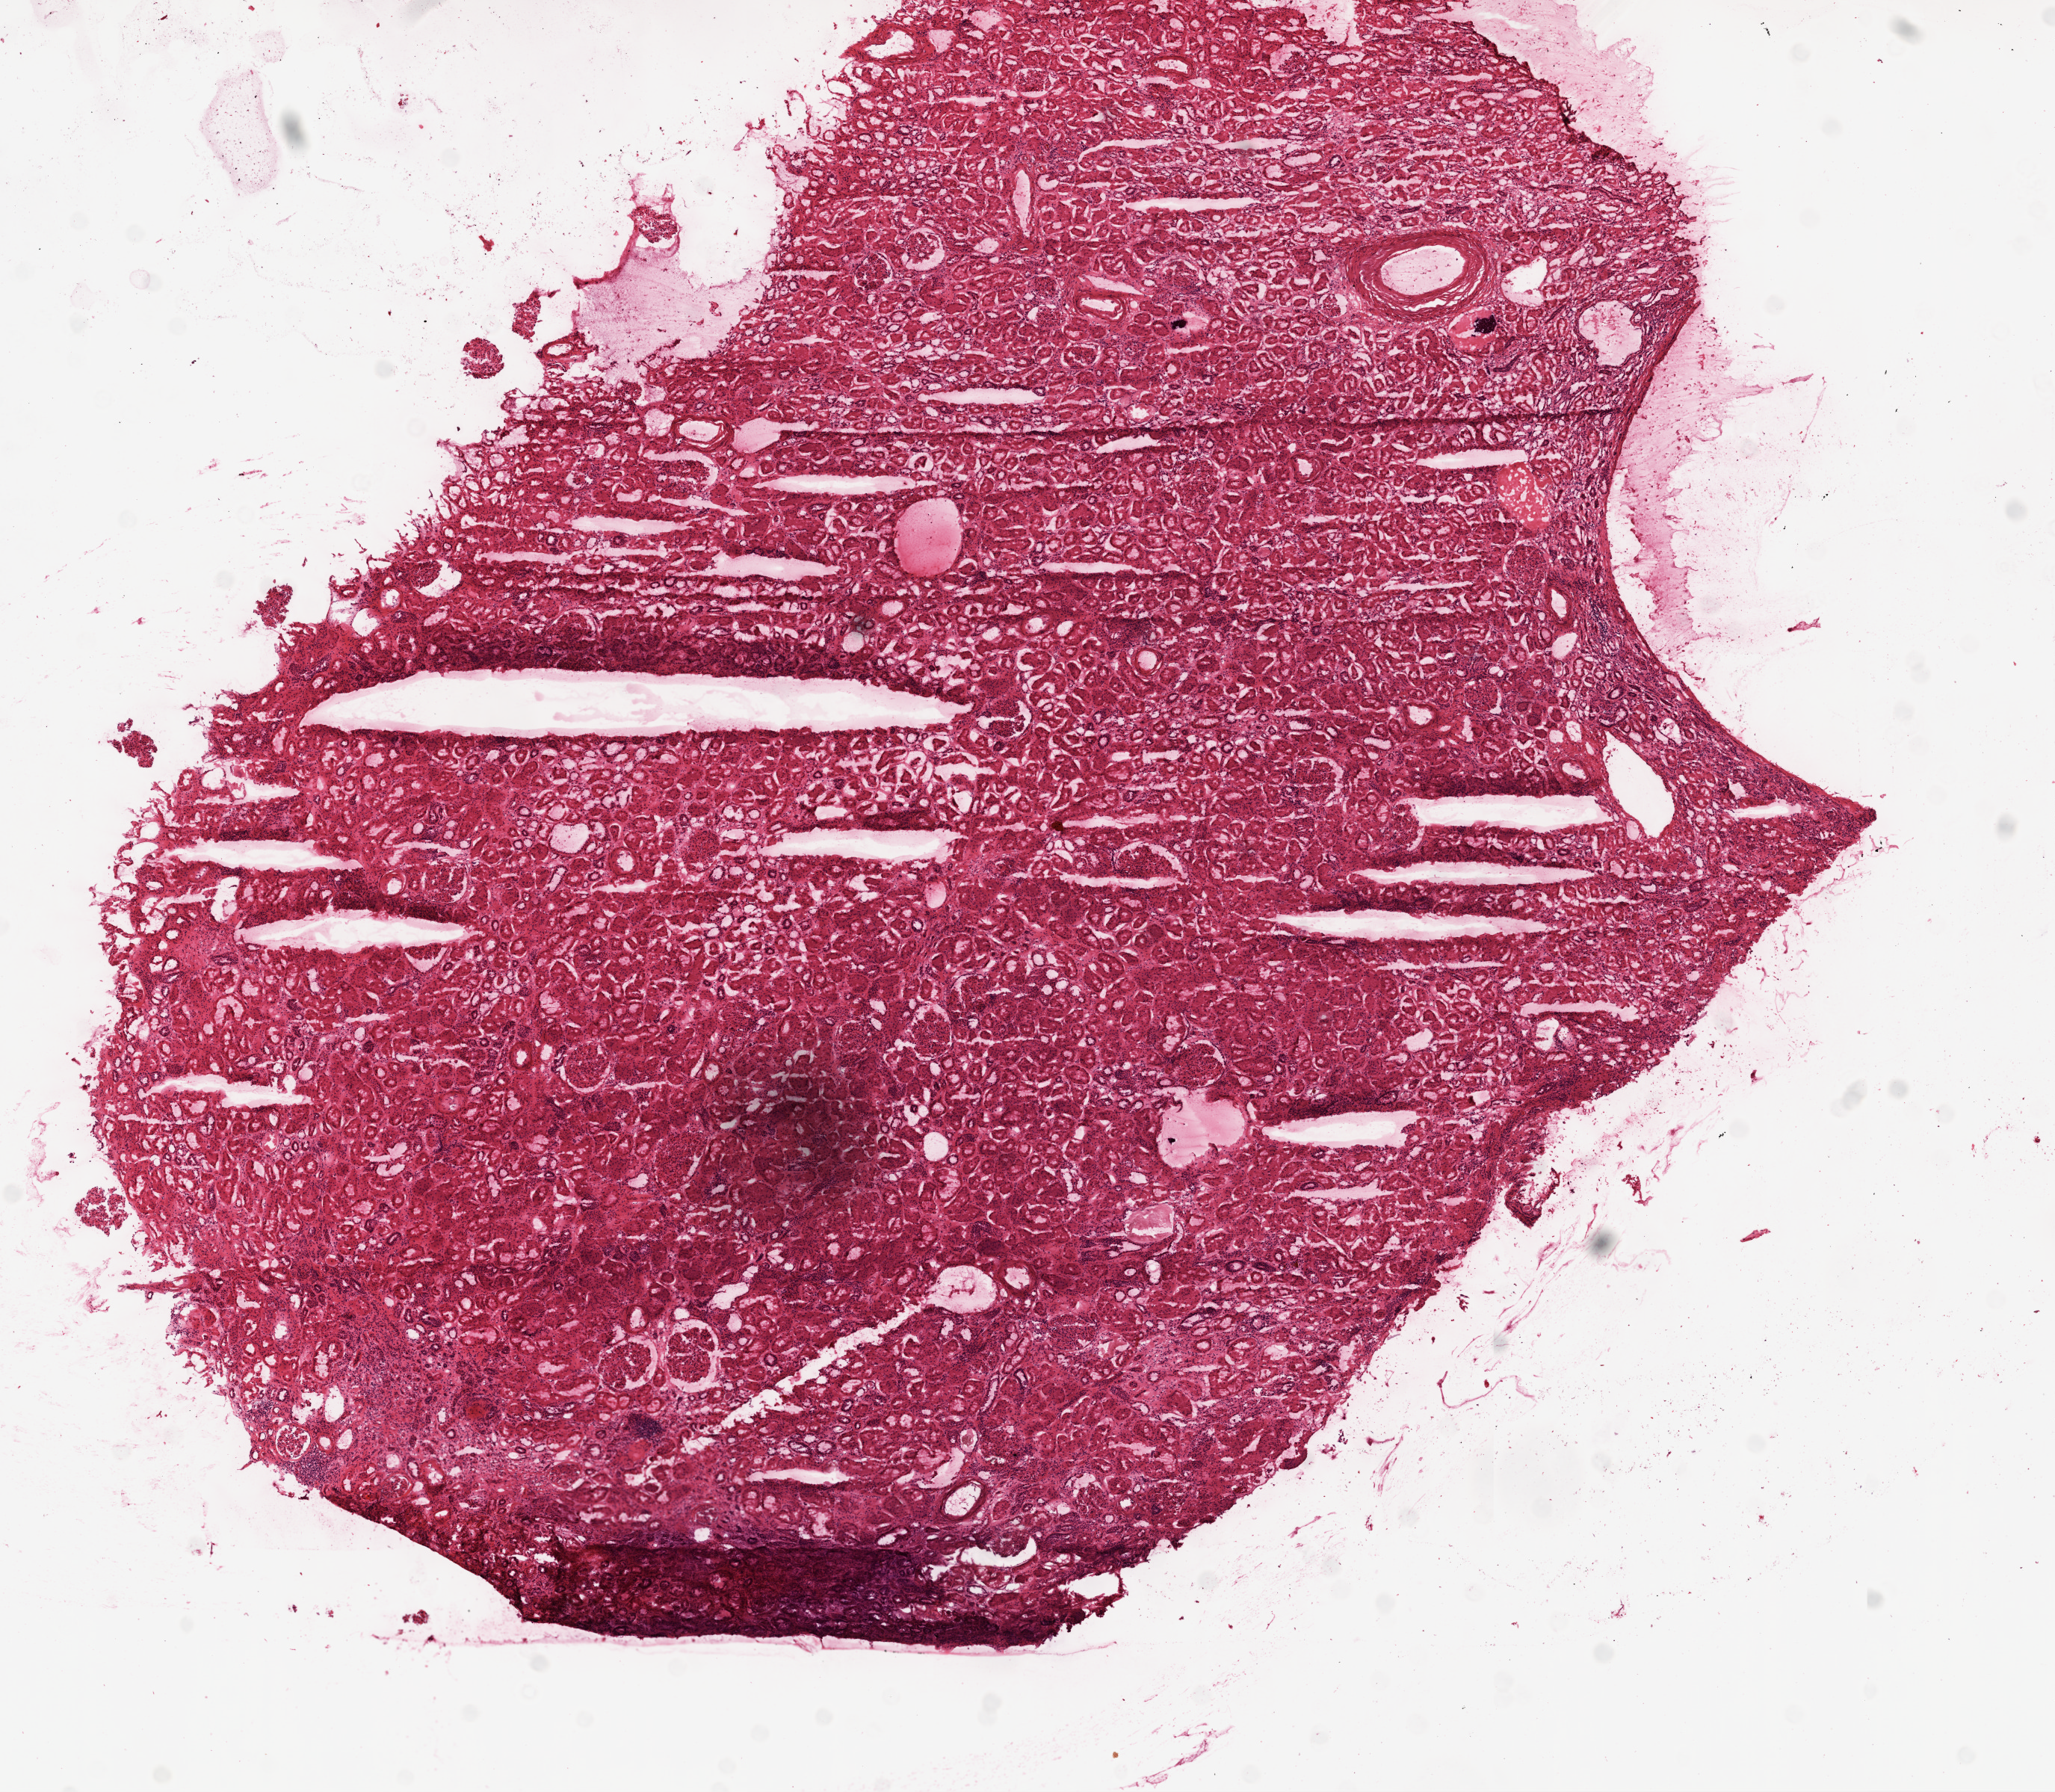
Hematoxylin and eosin (H&E) stained whole-slide image — shown as a low-resolution overview of the whole scanned area (about 11.0 x 9.6 mm, slide scanned at 20x), frozen section from the top of the tissue portion, sample: solid tissue normal (non-tumour tissue), kidney. Patient: female, age at initial diagnosis 76 years.
- this section: solid tissue normal (non-tumour) sample from the same patient
- patient diagnosis: Clear cell adenocarcinoma, NOS